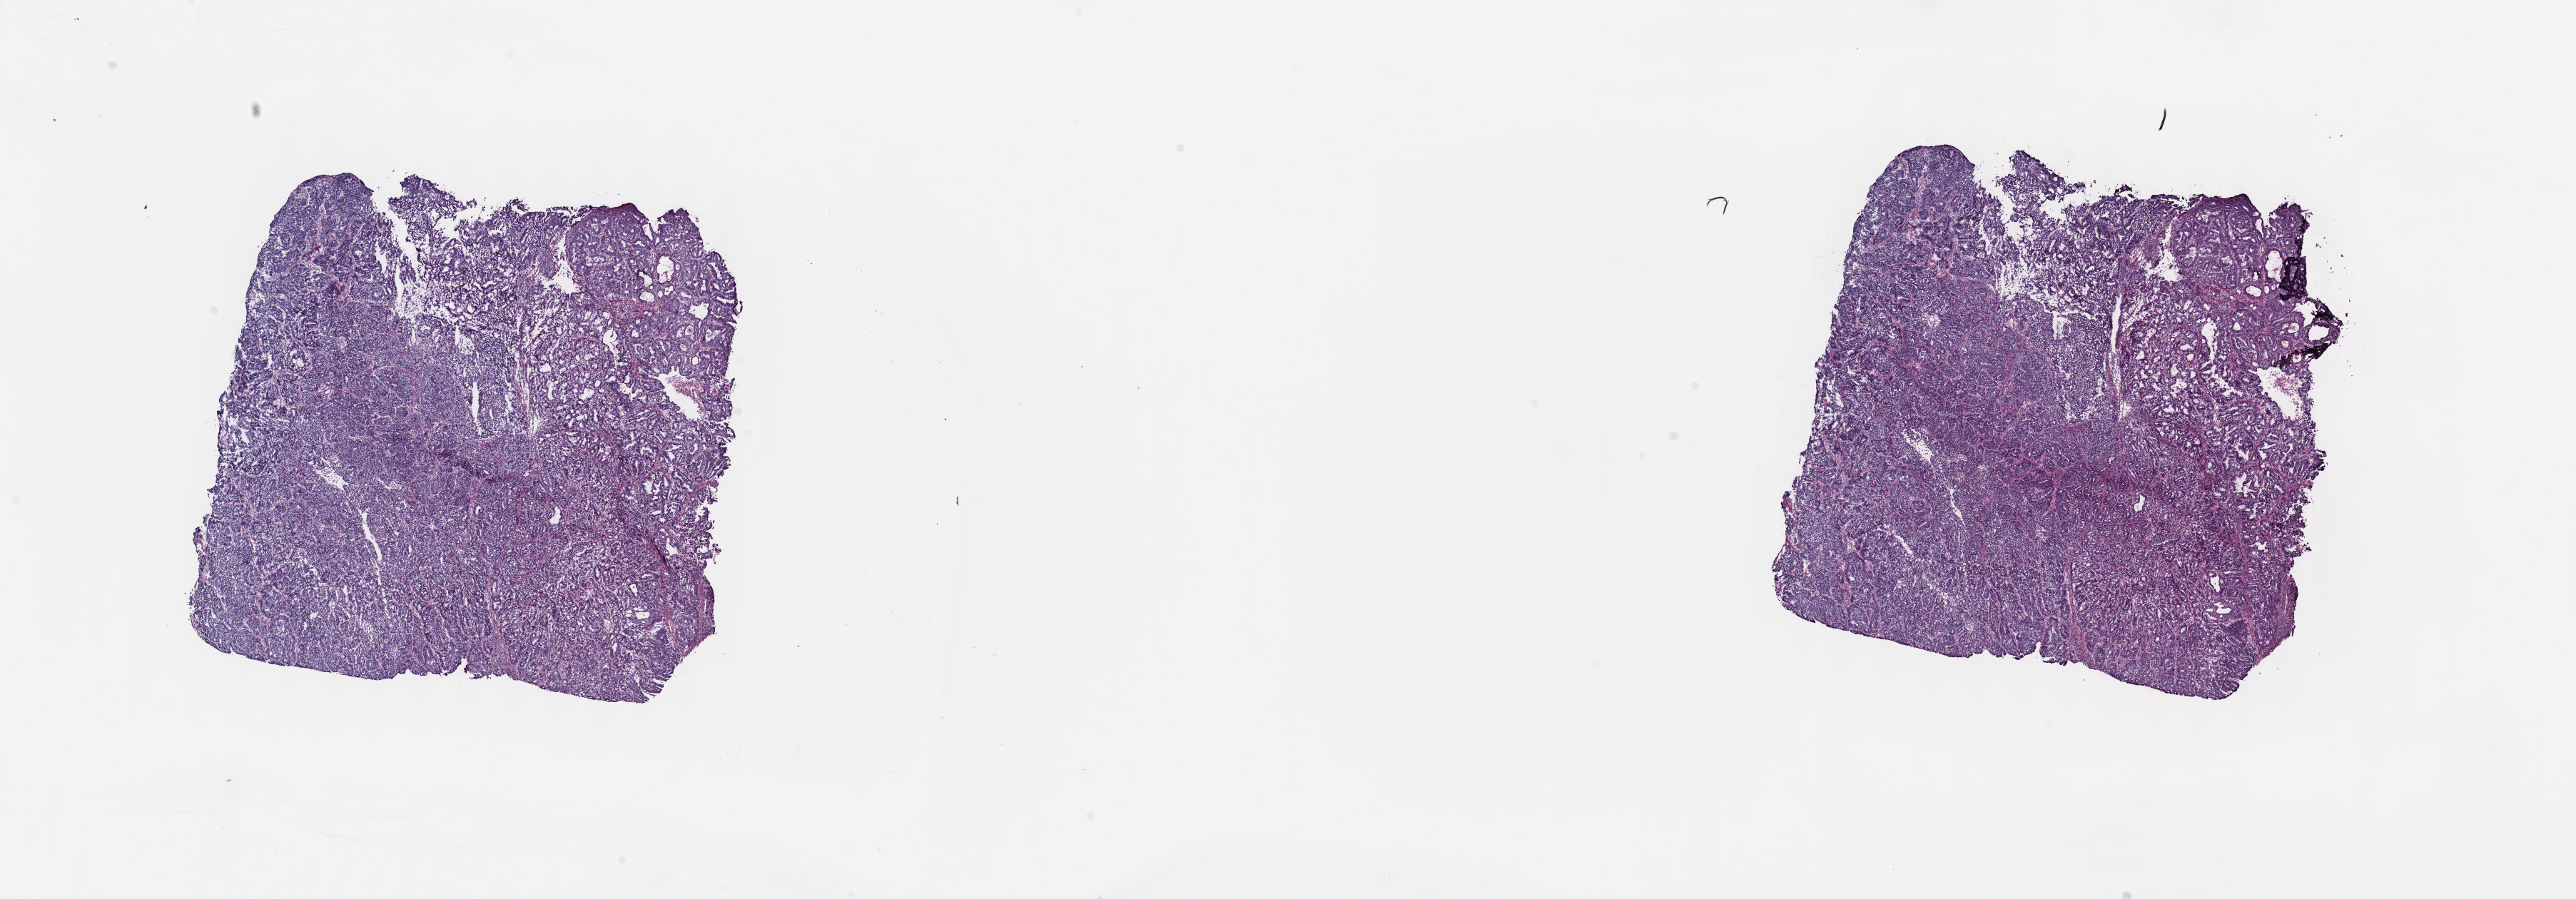
Digitized H&E tissue section (whole slide), shown as a low-resolution overview of the whole scanned area (about 29.2 x 10.2 mm), frozen section, sample: primary tumour, uterus. Female, age 64 years at initial diagnosis. Histologic grade: G2 (moderately differentiated). Pathologist review of this section (percent, as recorded): tumour cells 85%, tumour nuclei 85%, normal cells 5%, stromal cells 8%, necrosis 2%. Inflammatory infiltration, as recorded: lymphocyte infiltration 3%, monocyte infiltration 0%, neutrophil infiltration 0%.
FIGO stage: IA. Histologic diagnosis: Endometrioid adenocarcinoma, NOS (endometrium).